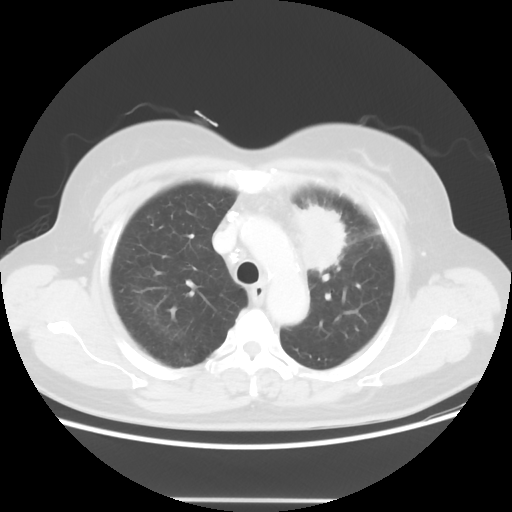
Chest CT, one axial slice; position 41 of 52 along the scan axis; 120 kVp; lung window (W 1500 / L -600 HU); 512 × 512 image matrix, field of view 382 × 382 mm. Patient: female, 52 years. From the clinical record (not read from this slice): clinical TNM (as recorded): T2 N3 M0.
Annotated regions visible in this slice (rectangle marked by the reading radiologist):
- lung tumour (recorded histology: adenocarcinoma): box from (x=285, y=196) to (x=347, y=277) px